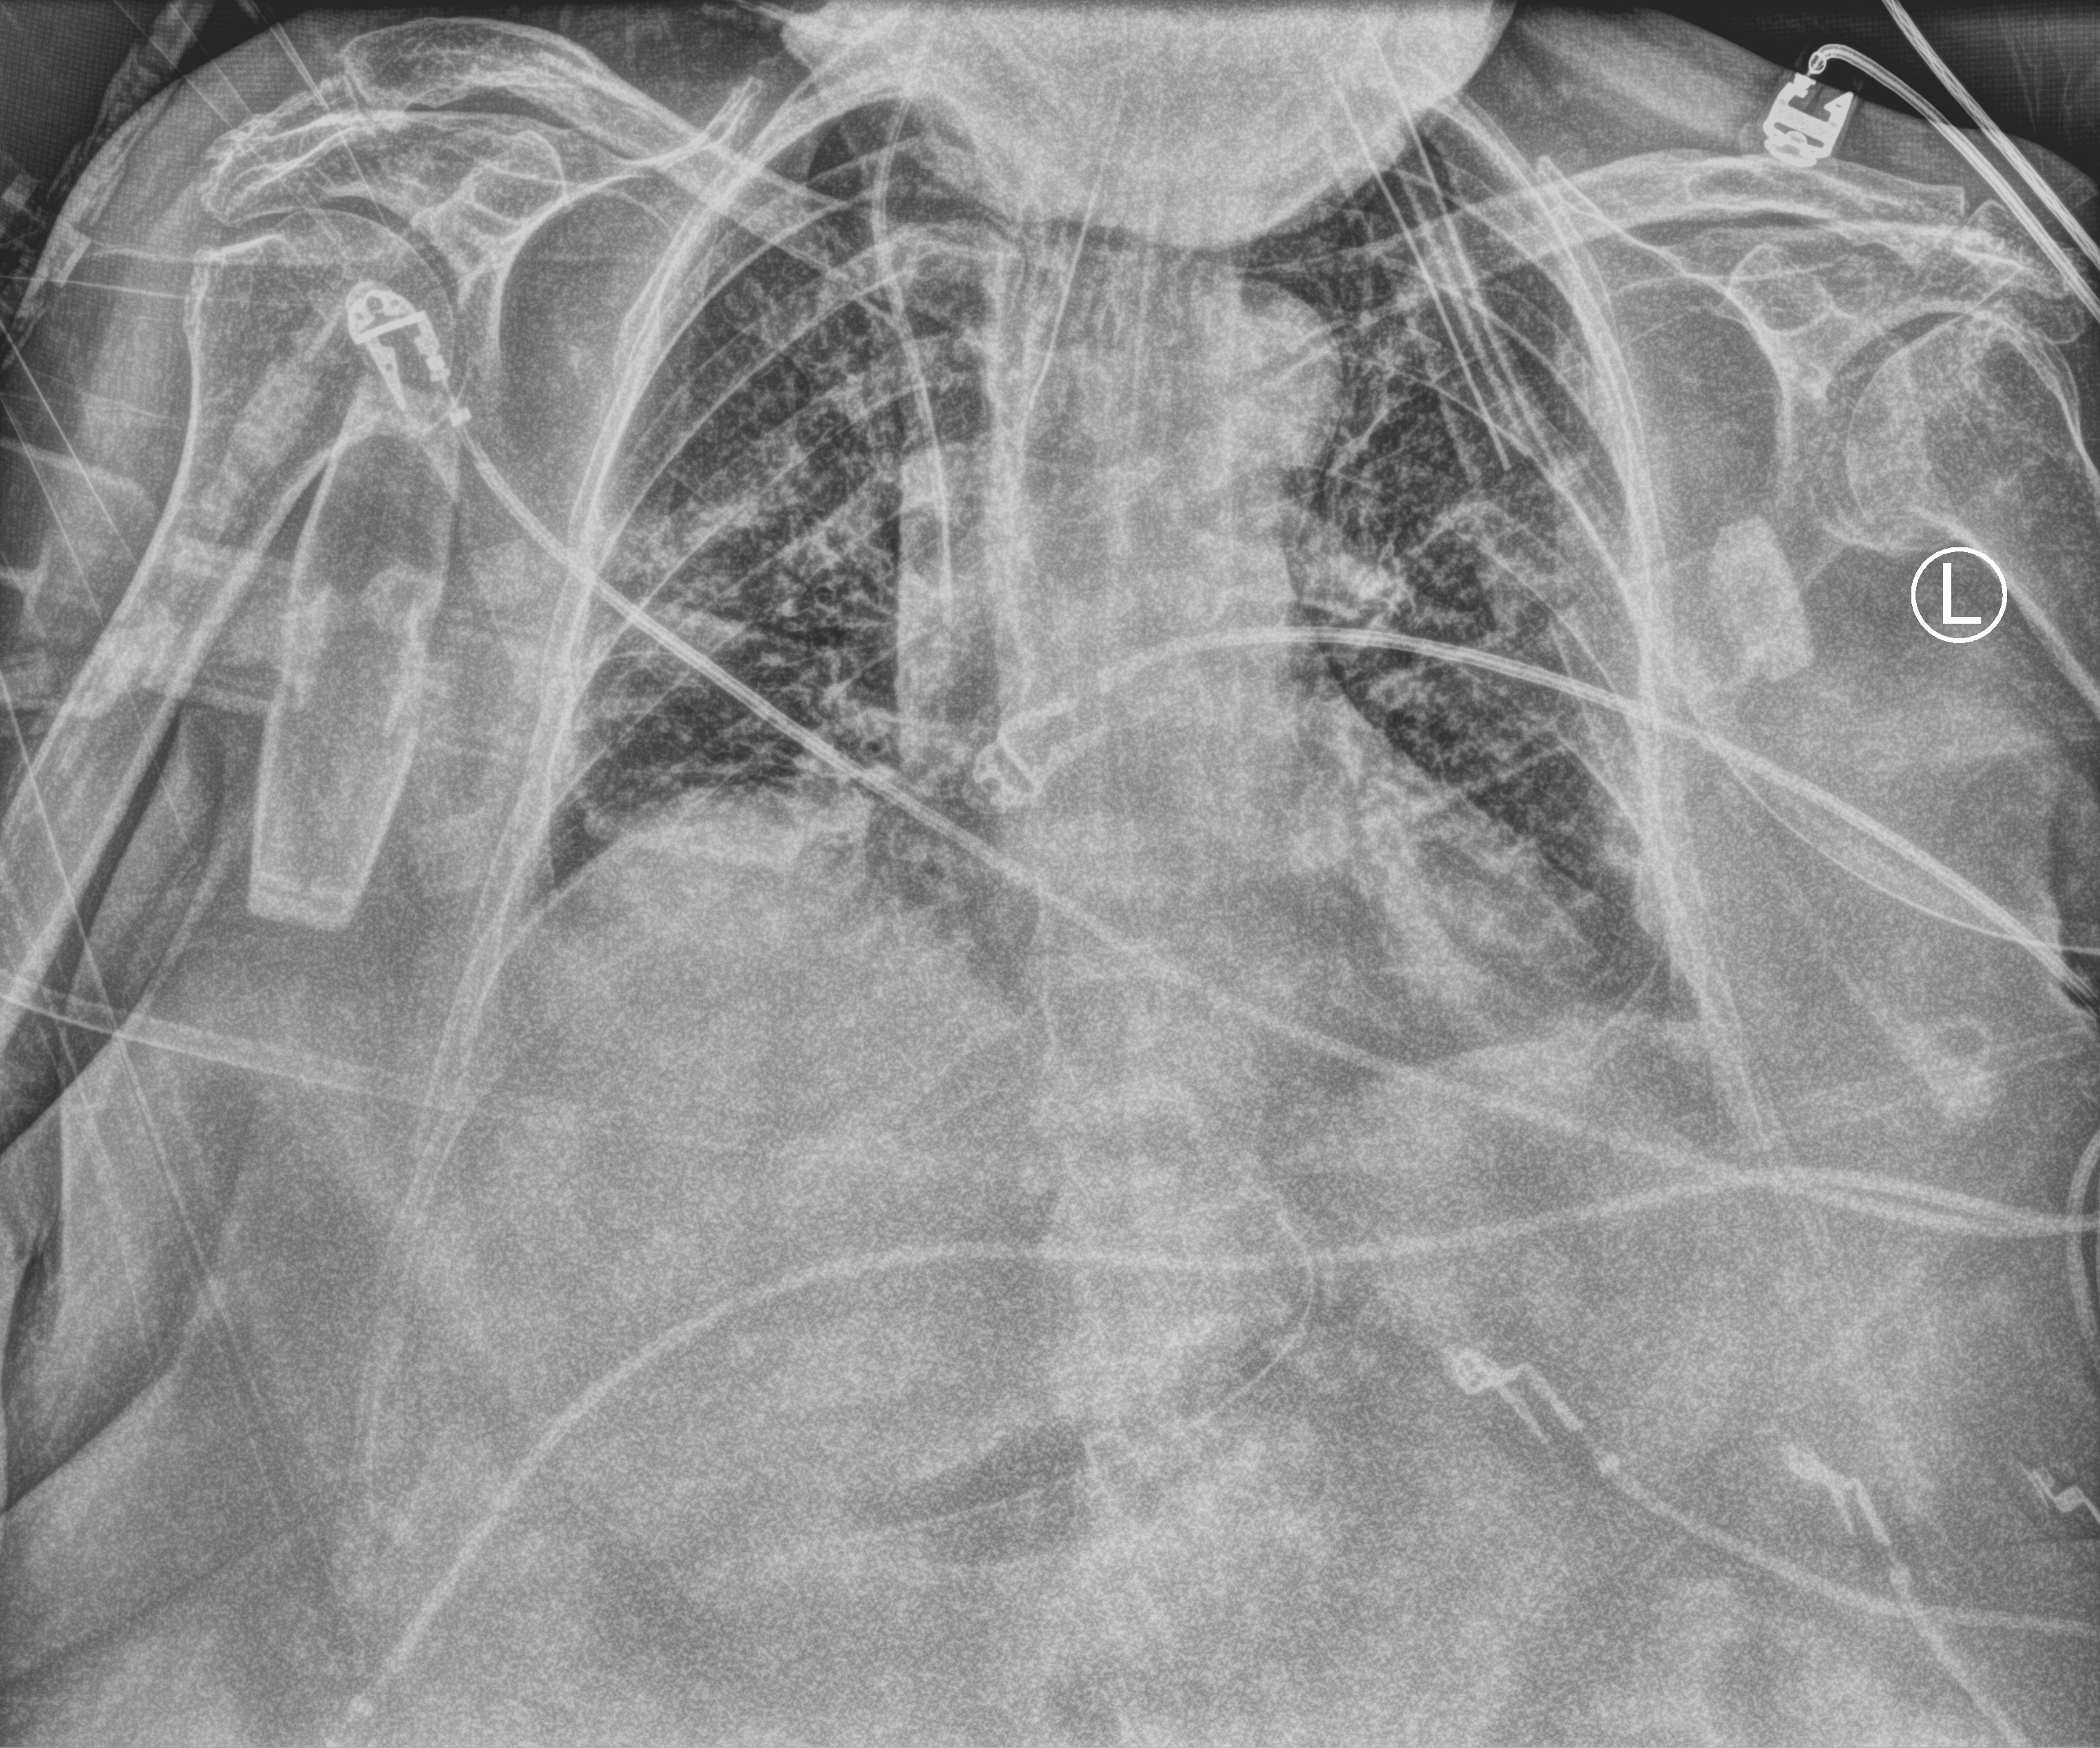
Chest X-ray (portable), anteroposterior (AP) projection. Patient hospitalised with COVID-19; female, aged 75–90 years.
Admission-level facts for this patient (not findings on this image; timing relative to this image not recorded):
- smoking status (admission record): never
- COPD (admission record): yes